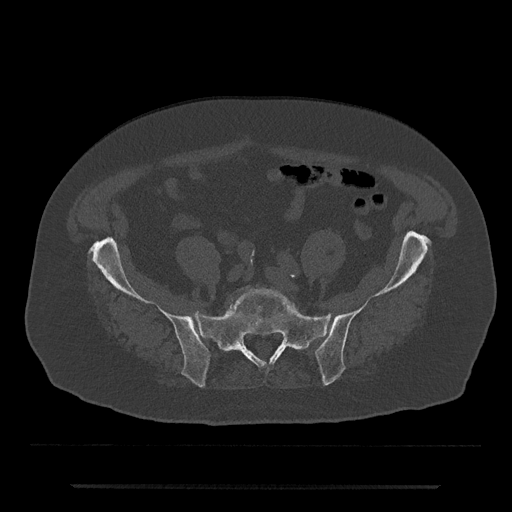
CT including the spine, one axial slice; position 243 of 797 along the scan axis; bone window (W 1800 / L 400 HU); 0.5 mm slice thickness; 512 × 512 image matrix, field of view 434 × 434 mm. Patient: male, 80 years. Case-level facts recorded for this patient, not image findings: primary cancer: prostate; vertebrae with lytic lesions (as recorded): L1, T11.
Structures marked on this image (semi-automatic segmentation, software-assisted and operator-edited):
- L5 vertebra: bounding box [x1, y1, x2, y2] px = [229, 288, 299, 315]